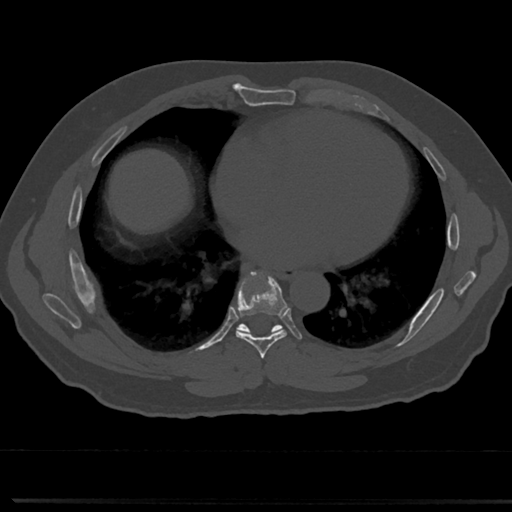
CT including the spine, one axial slice. Slice 390 of 817 in the series (ordered by position). Reconstruction kernel Br40s/3. Bone window (W 1800 / L 400 HU). 0.5 mm slice thickness. 512 × 512 image matrix, field of view 355 × 355 mm. Patient: male, 61 years. From the clinical record (not read from this slice): primary cancer: prostate.
Structures marked on this image (semi-automatically segmented with operator editing):
- T6 vertebra: bounding box <260,360,269,377> (left, top, right, bottom; pixels)
- T7 vertebra: <215,275,310,356>